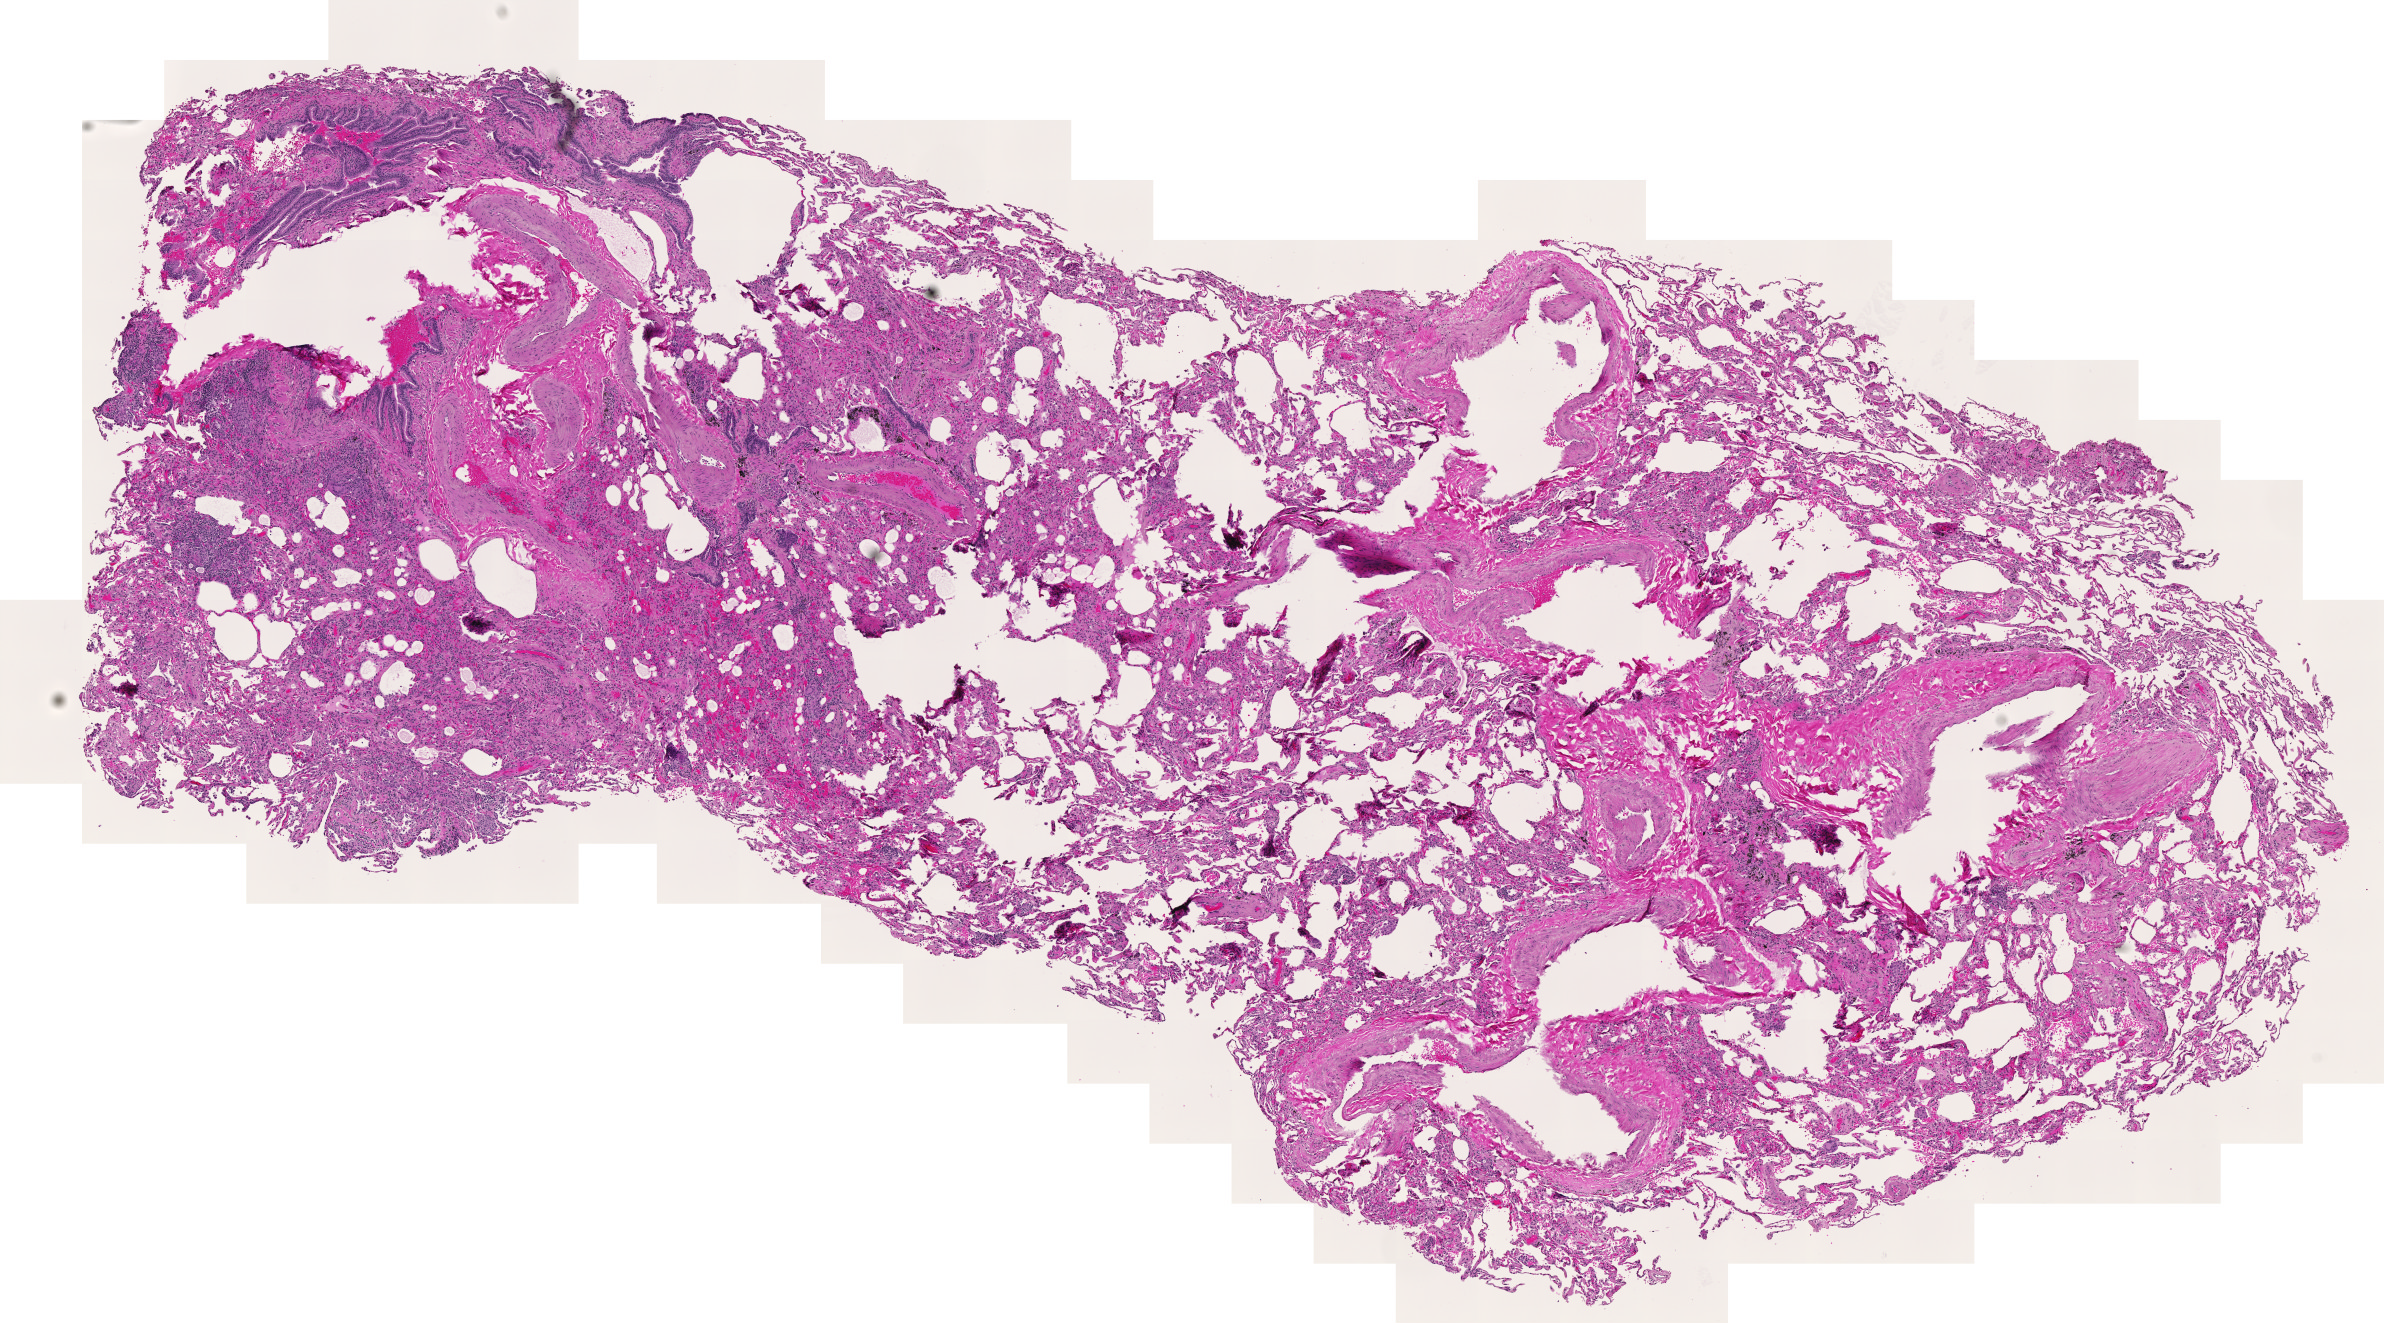
Whole-slide histology image, H&E-stained — low-resolution overview of the scanned area, about 12.3 x 6.8 mm. Normal (non-tumour) tissue sample, lung. 73-year-old male patient.
This section: normal (non-tumour) tissue from the same patient. Patient diagnosis: Adenocarcinoma, NOS.